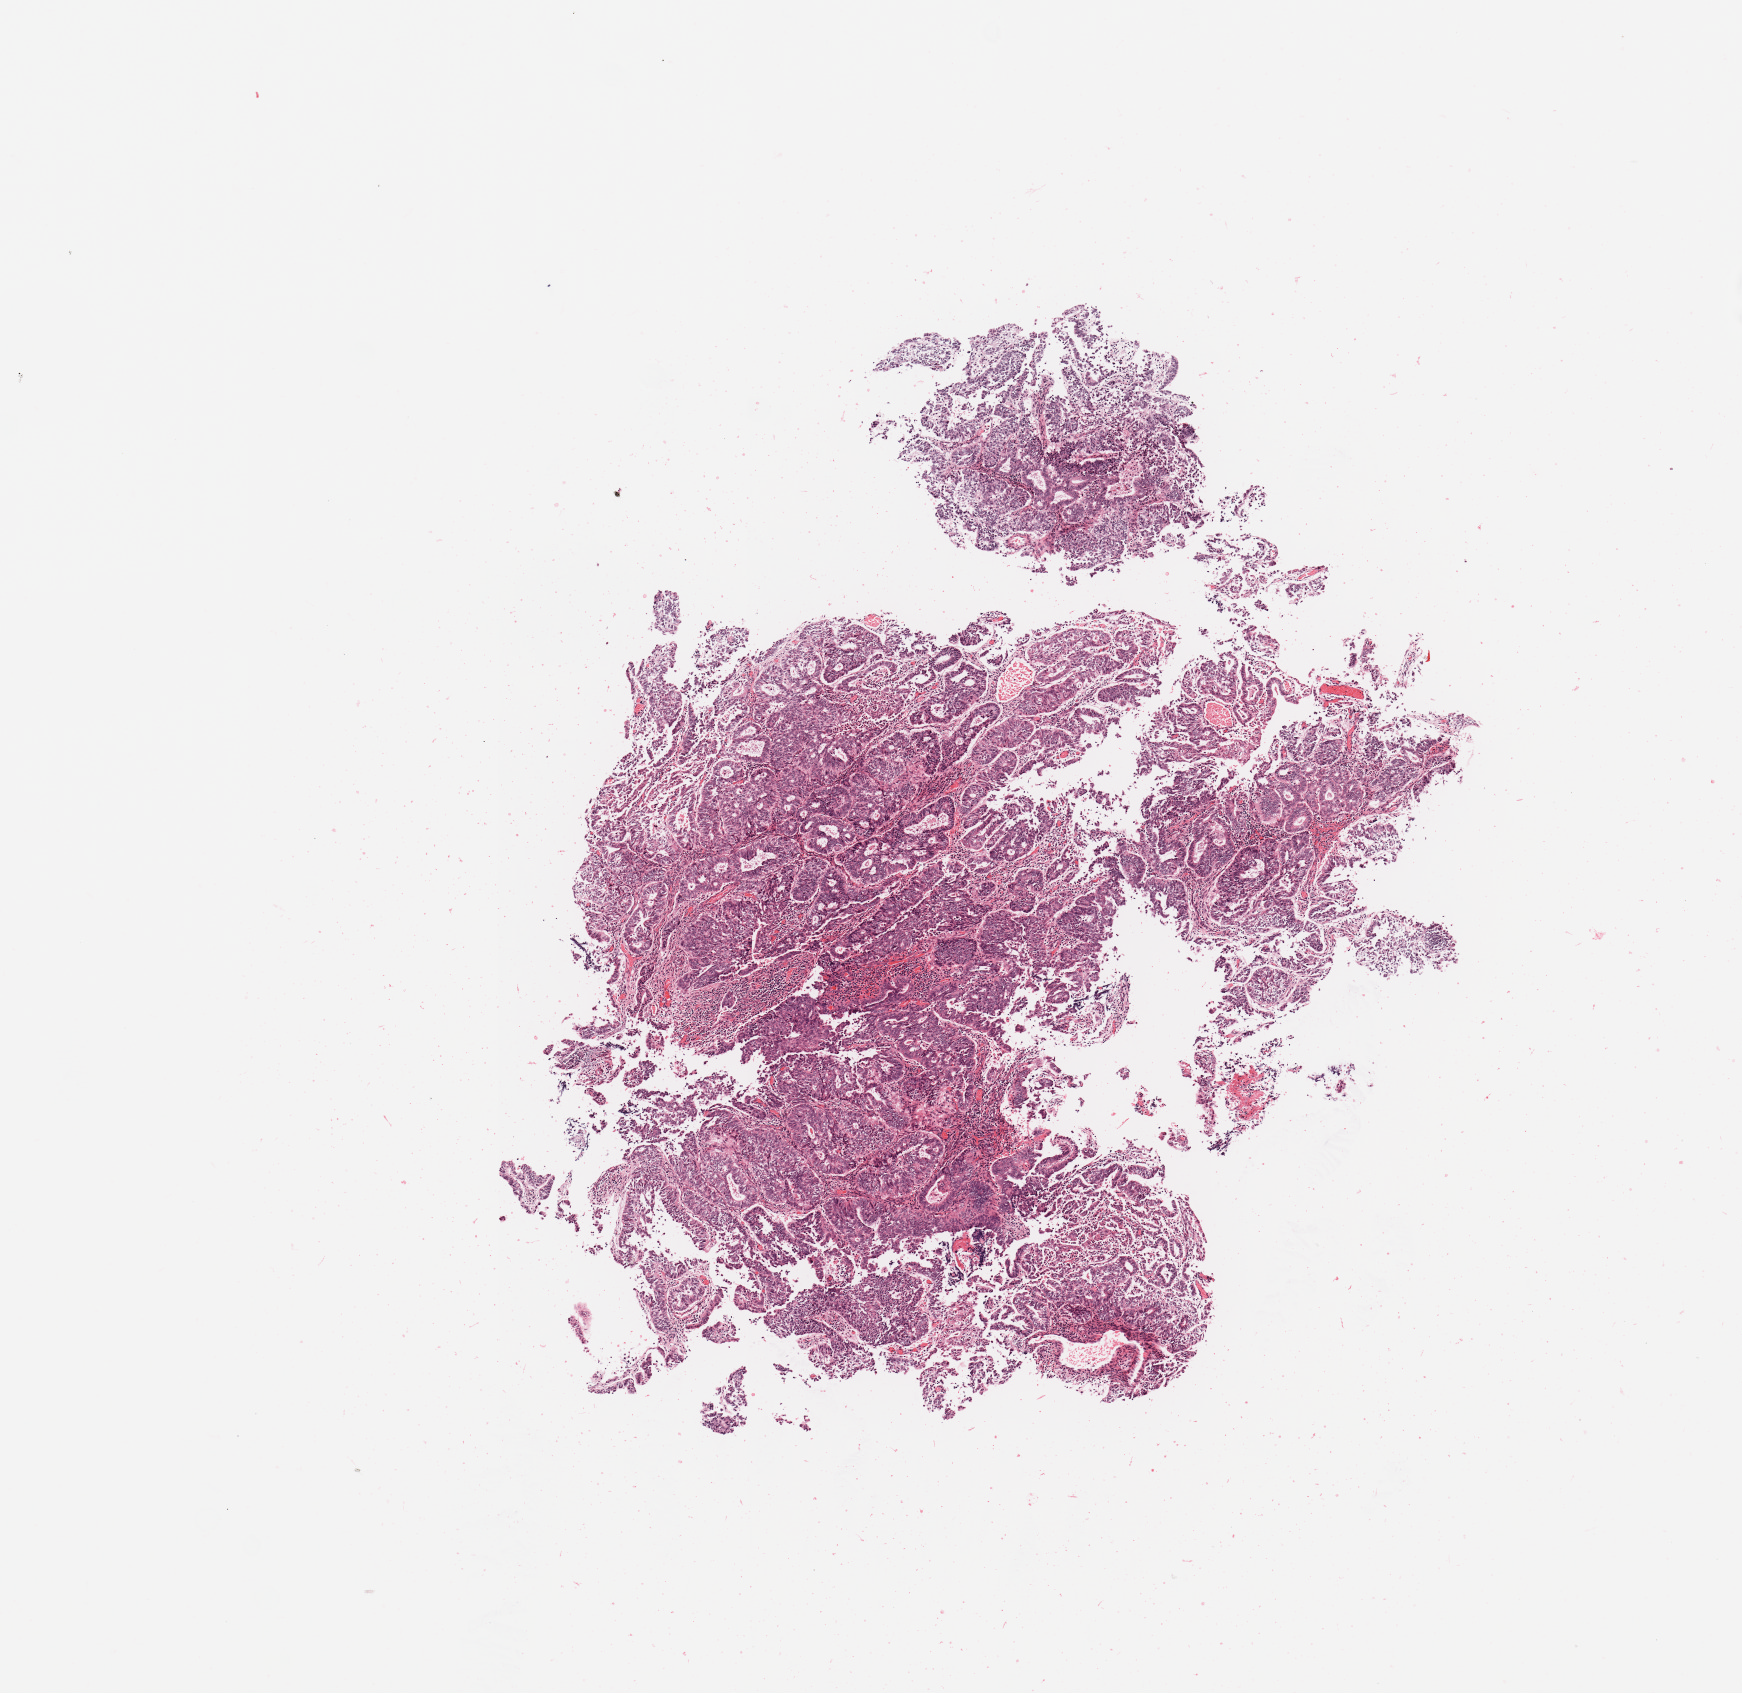
Whole-slide histology image, H&E-stained — a low-resolution overview of the entire scanned area, about 6.9 x 6.7 mm (acquisition: 20x scan). Tumour tissue sample, uterus. Female, 60 y/o. Histologic grade: G2 (moderately differentiated).
AJCC pathologic stage: I. Diagnosis: Endometrioid adenocarcinoma, NOS.